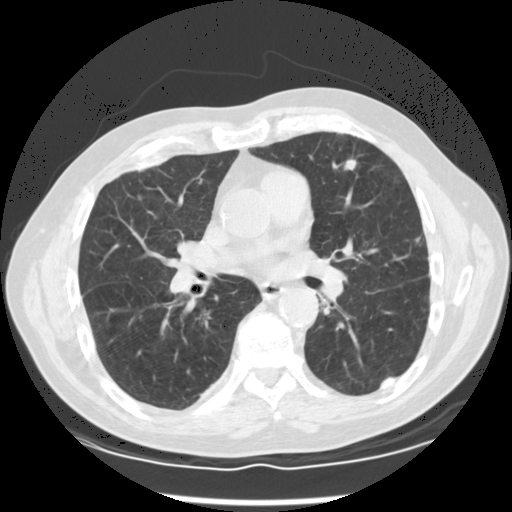
Low-dose screening chest CT, axial slice. Third annual screen. Lung window (W 1500 / L -600 HU). 2.5 mm slice thickness. Slice 64 of 120 in the series. Male, age 68 years at enrolment. Former smoker at enrolment.
- Expert reader's lesion annotation, box from (x=325, y=148) to (x=371, y=191) px.
- Screening reader's record for this exam (one nodule recorded; not confirmed to be the boxed lesion): non-calcified nodule or mass ≥4 mm, left upper lobe, 10 × 8 mm, spiculated (stellate) margins, soft tissue attenuation, pre-existing on the prior screen: no.
- Later outcome: lung cancer diagnosed 53 days after this screen — squamous cell carcinoma, NOS, left upper lobe, moderately differentiated (G2), stage IA (AJCC 6th edition), 17 mm at pathology.